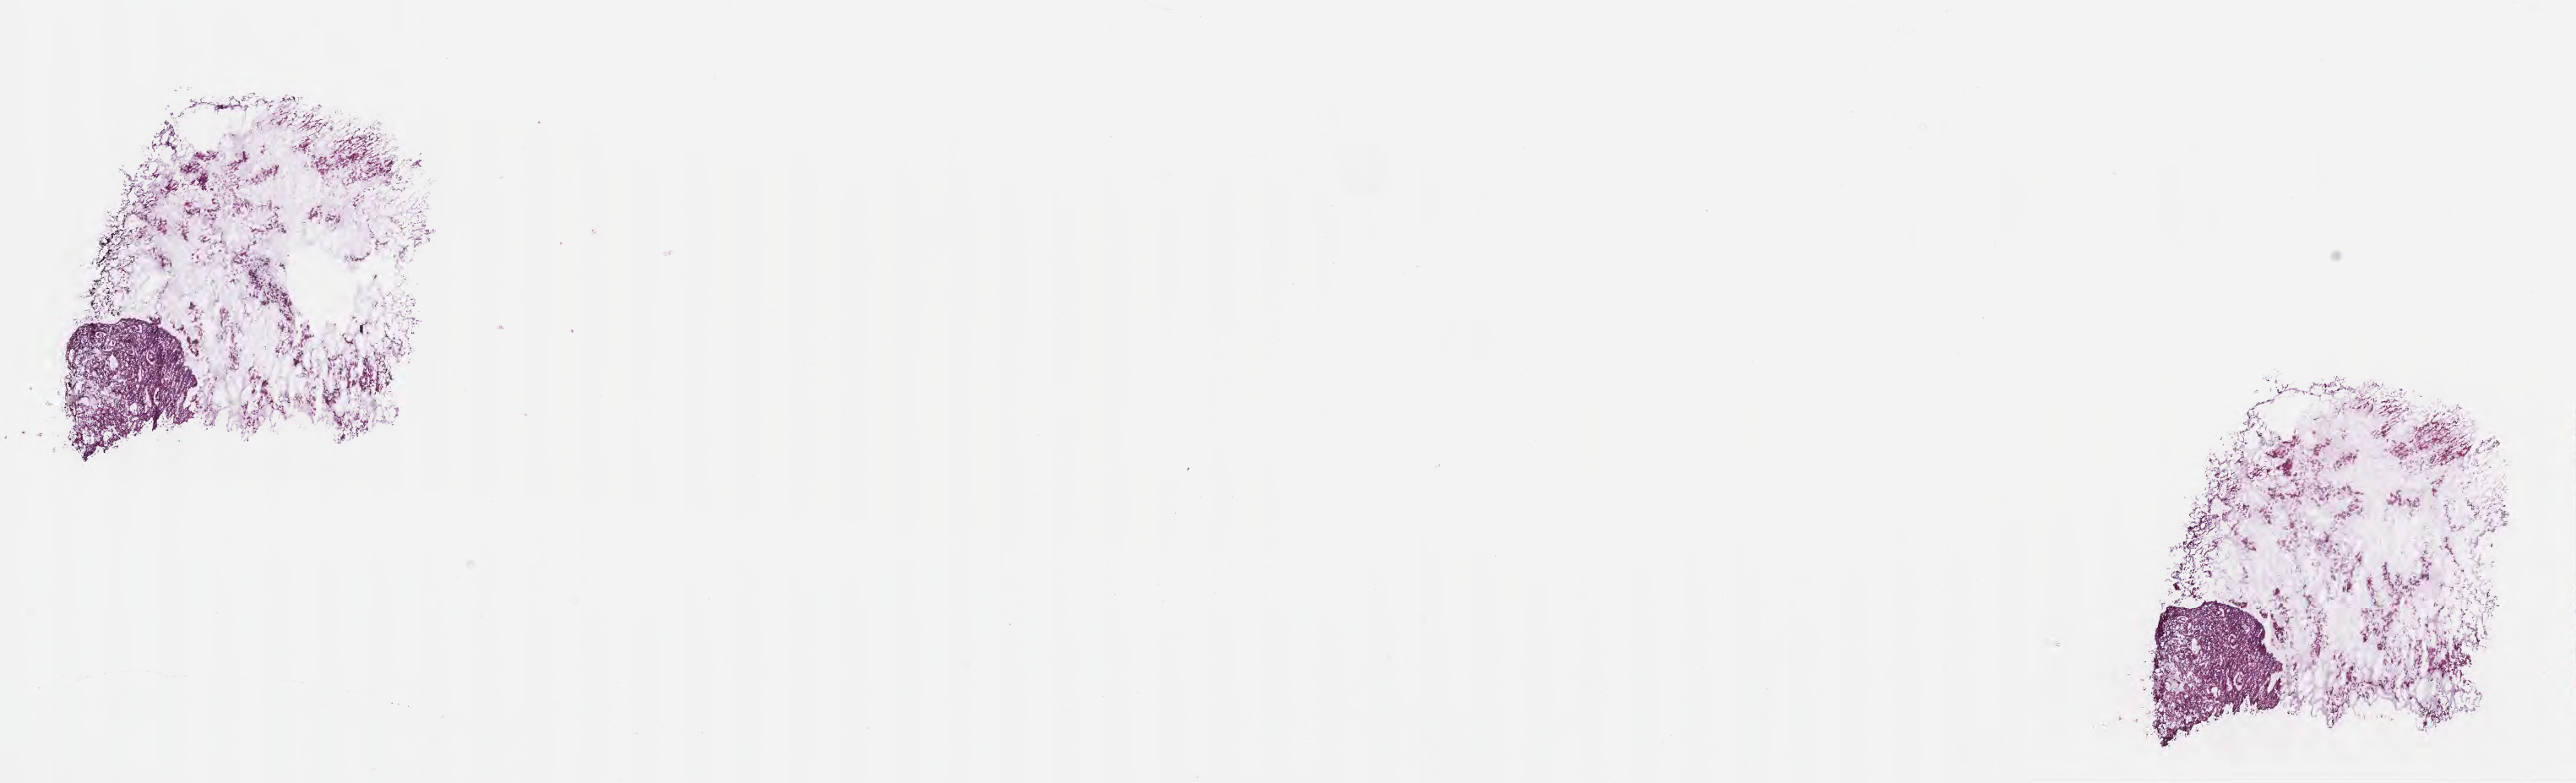
Digitized hematoxylin and eosin (H&E)-stained section, shown as a low-resolution overview of the whole scanned area (about 24.6 x 7.5 mm), frozen section (tissue freezing medium), primary tumor, site: hepatic flexure of colon. Male patient; age at initial diagnosis 69 years. Tumor grade: G2 (moderately differentiated). Pathologist review of this section (percent, as recorded): tumor cells 80%, tumor nuclei 80%, stromal cells 18%, necrosis 2%, normal cells 0%. Inflammatory infiltration, as recorded: lymphocyte infiltration 4%, monocyte infiltration 2%, neutrophil infiltration 6%.
Histologic diagnosis: Mucinous adenocarcinoma. Section: top of the tissue portion. AJCC pathologic stage: Stage IIIC.